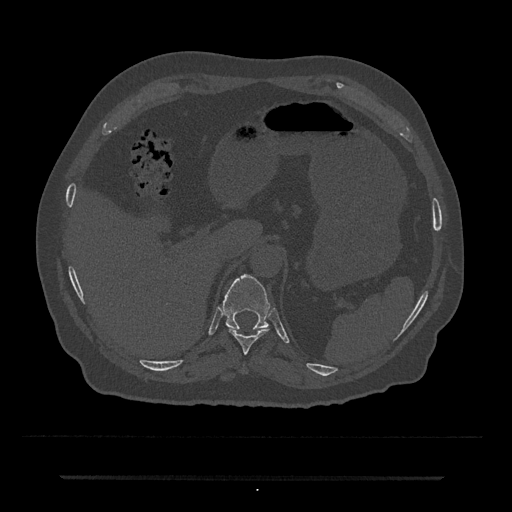
CT including the spine, one axial slice; slice 205 of 797 in the series (ordered by position); reconstruction kernel Br40s/3; bone window (W 1800 / L 400 HU); 0.5 mm slice thickness; 512 × 512 image matrix, field of view 437 × 437 mm. Patient: male, 69 years. From the clinical record (not read from this slice): primary cancer: prostate.
Structures marked on this image (semi-automatically segmented with operator editing):
- T10 vertebra: bounding box [x1, y1, x2, y2] px = [228, 327, 268, 354]
- T11 vertebra: [223, 274, 270, 330]